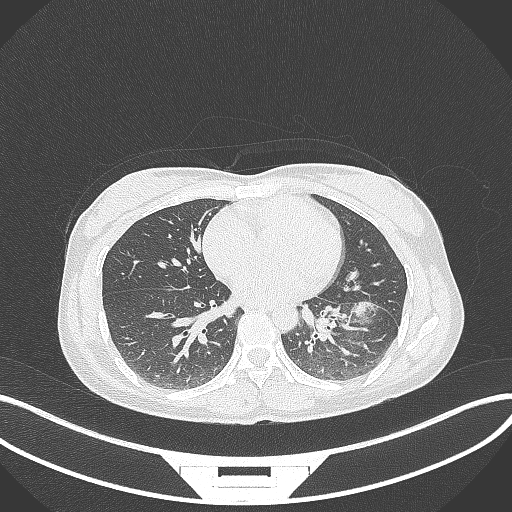
Chest CT, one axial slice; slice 36 of 244 in the series (ordered by position); reconstruction kernel B70f; lung window (W 1500 / L -600 HU); 512 × 512 image matrix, field of view 400 × 400 mm. Female patient, age 41 years. From the clinical record (not read from this slice): clinical TNM (as recorded): T2a N3 M1b.
Annotated regions visible in this slice (rectangle marked by the reading radiologist):
- lung tumour (recorded histology: adenocarcinoma): box from (x=351, y=303) to (x=380, y=319) px